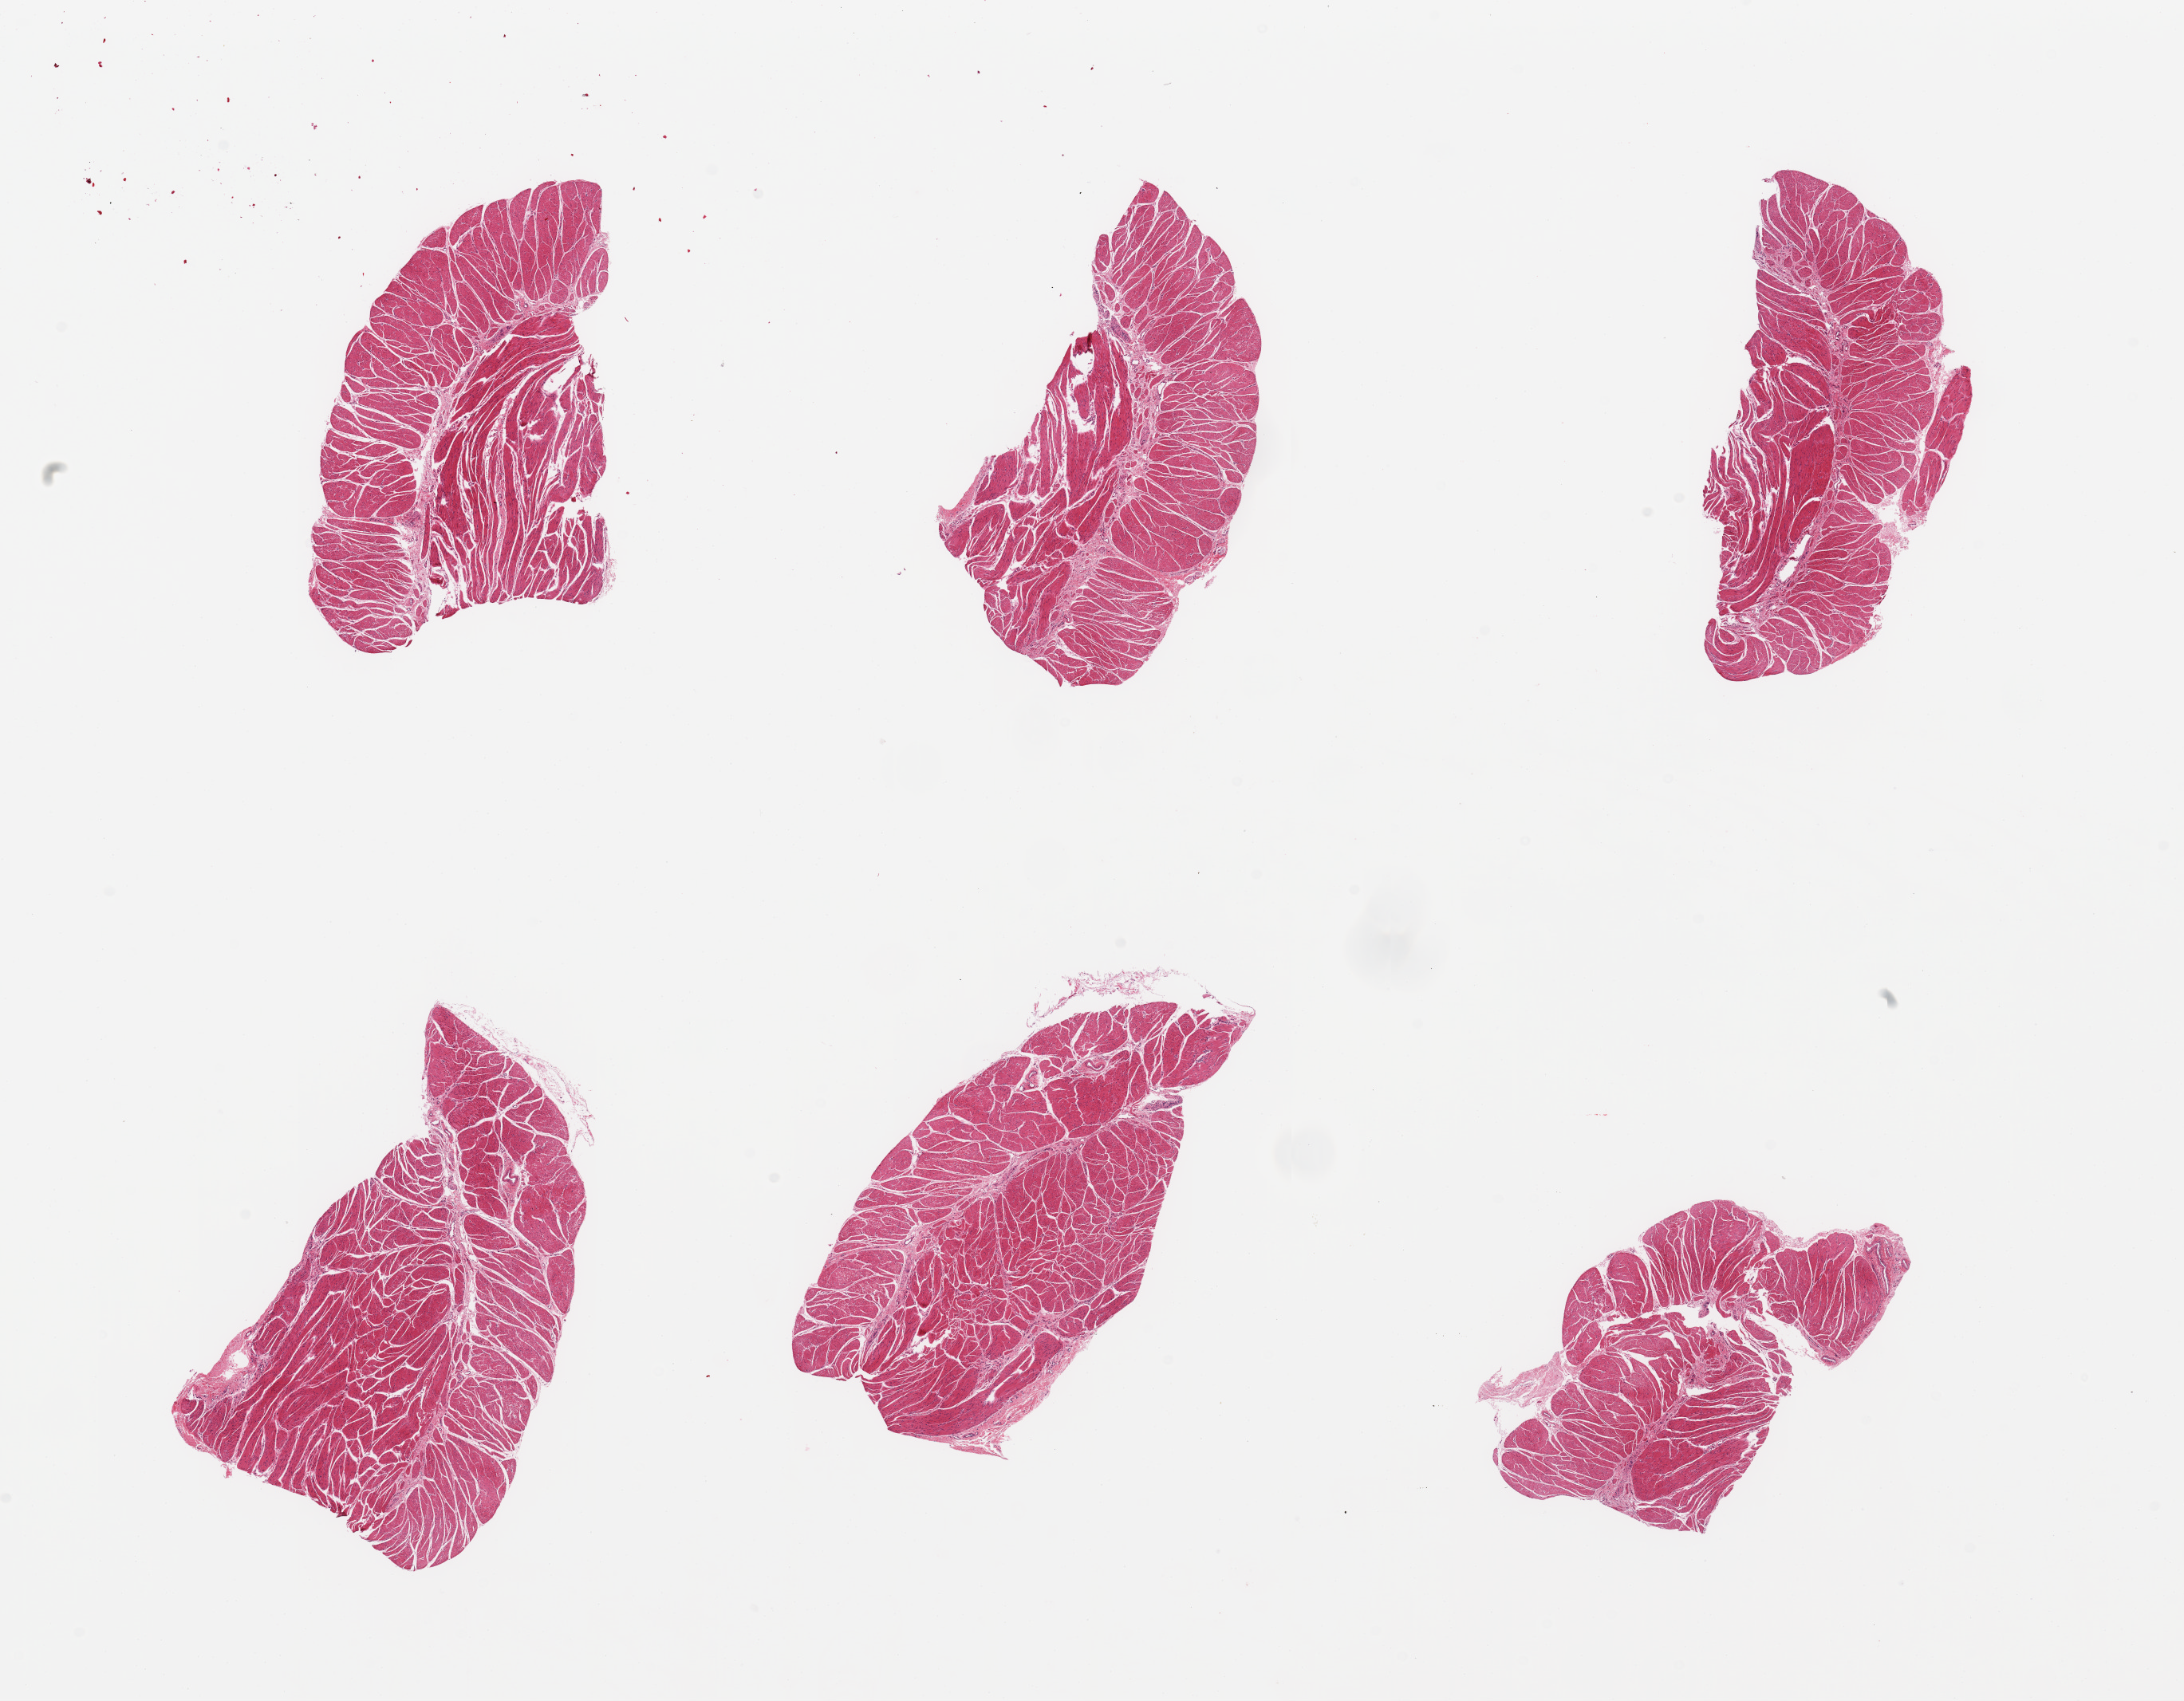
Digitized hematoxylin and eosin (H&E)-stained section — whole scanned area (about 21.7 x 16.9 mm) shown as a low-resolution overview. PAXgene-fixed, paraffin-embedded tissue. Sampled site (target tissue): esophageal muscle. Tissue donor sample. Donor: female.
Review note (as recorded): 6 pieces, confirmed target muscularis.